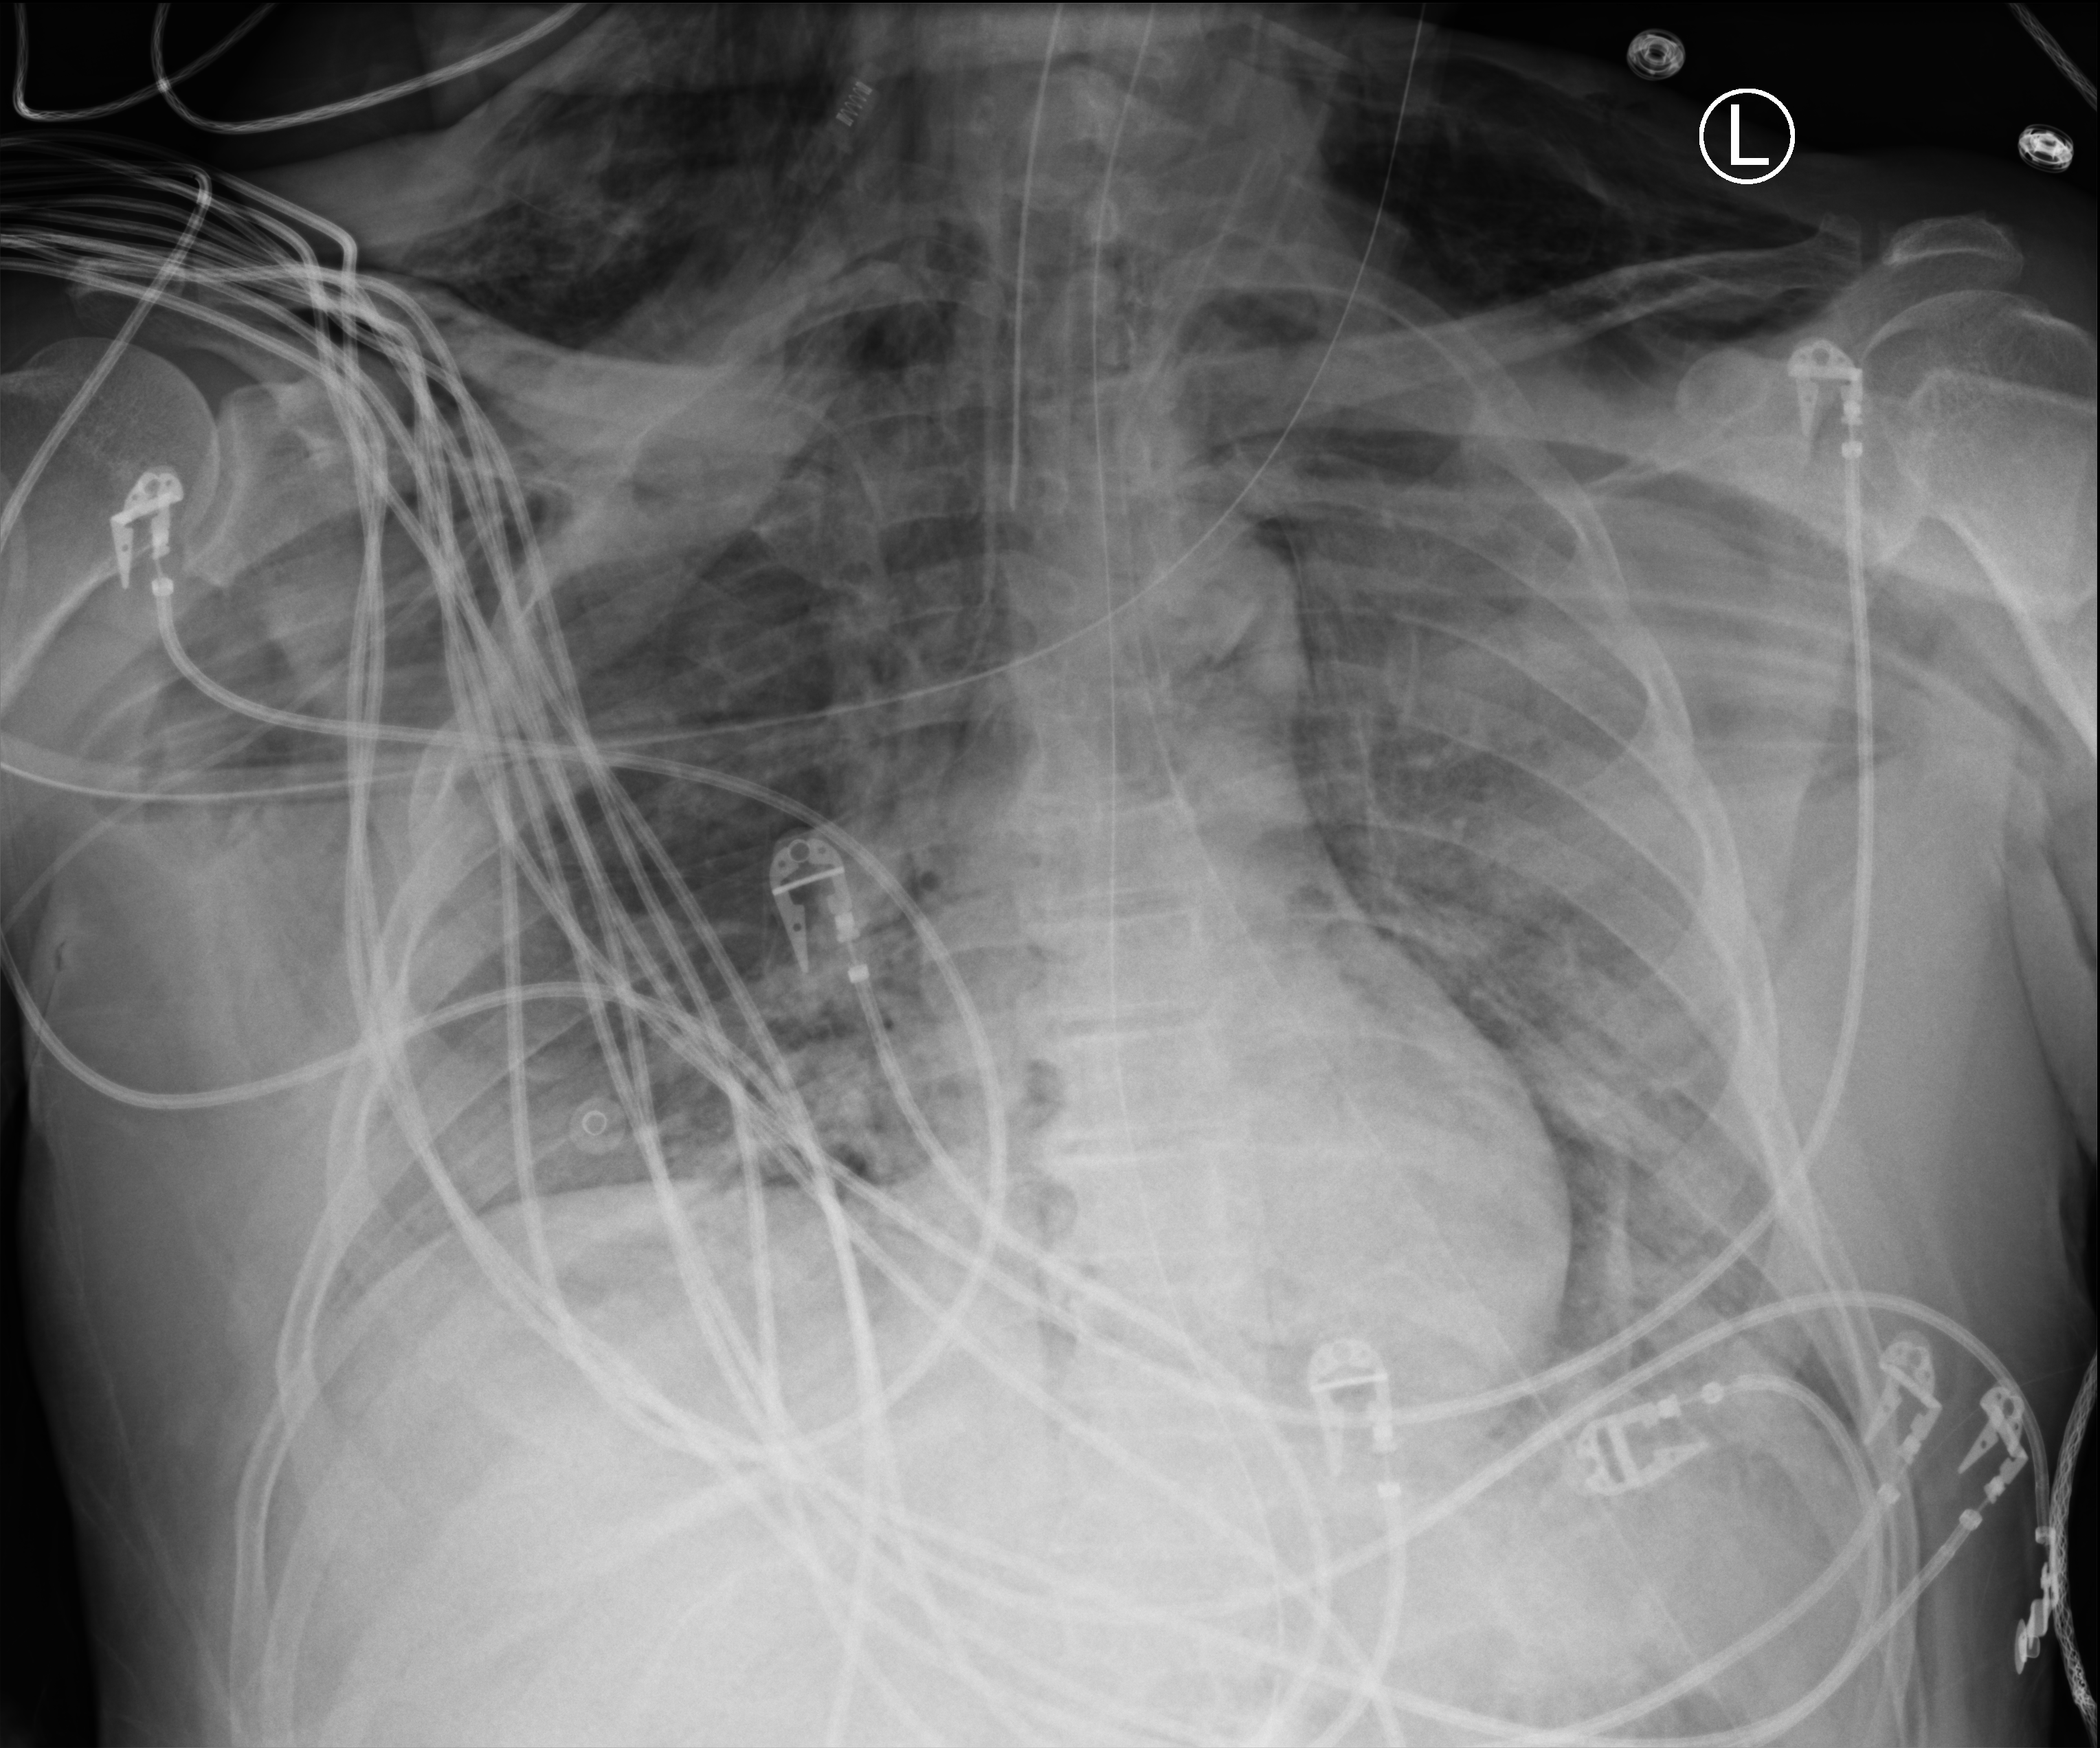
Portable chest radiograph, anteroposterior (AP) projection. Male patient hospitalised with COVID-19, age 18–59 years.
From the hospital-stay record, not from the radiograph (when in the stay this image was taken is not recorded): smoking status (admission record): never.